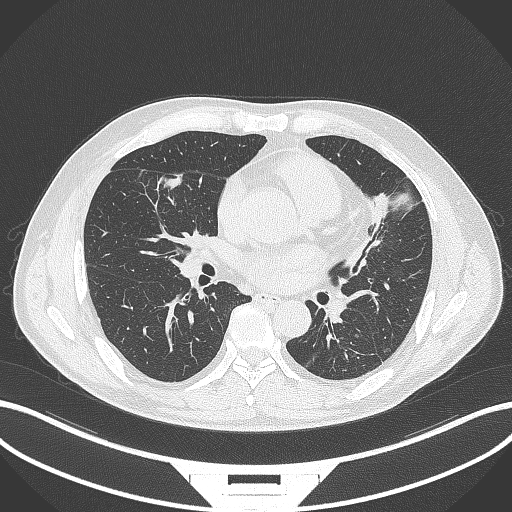
Chest CT, one axial slice. Position 151 of 399 along the scan axis. 120 kVp. Lung window (W 1500 / L -600 HU). 1 mm slice thickness. 512 × 512 image matrix, field of view 400 × 400 mm. Male patient, age 59 years. From the clinical record (not read from this slice): clinical TNM (as recorded): T2a N1 M0.
Annotated regions visible in this slice (rectangle marked by the reading radiologist):
- lung tumour (recorded histology: adenocarcinoma): bounding box [x1, y1, x2, y2] px = [159, 164, 188, 194]